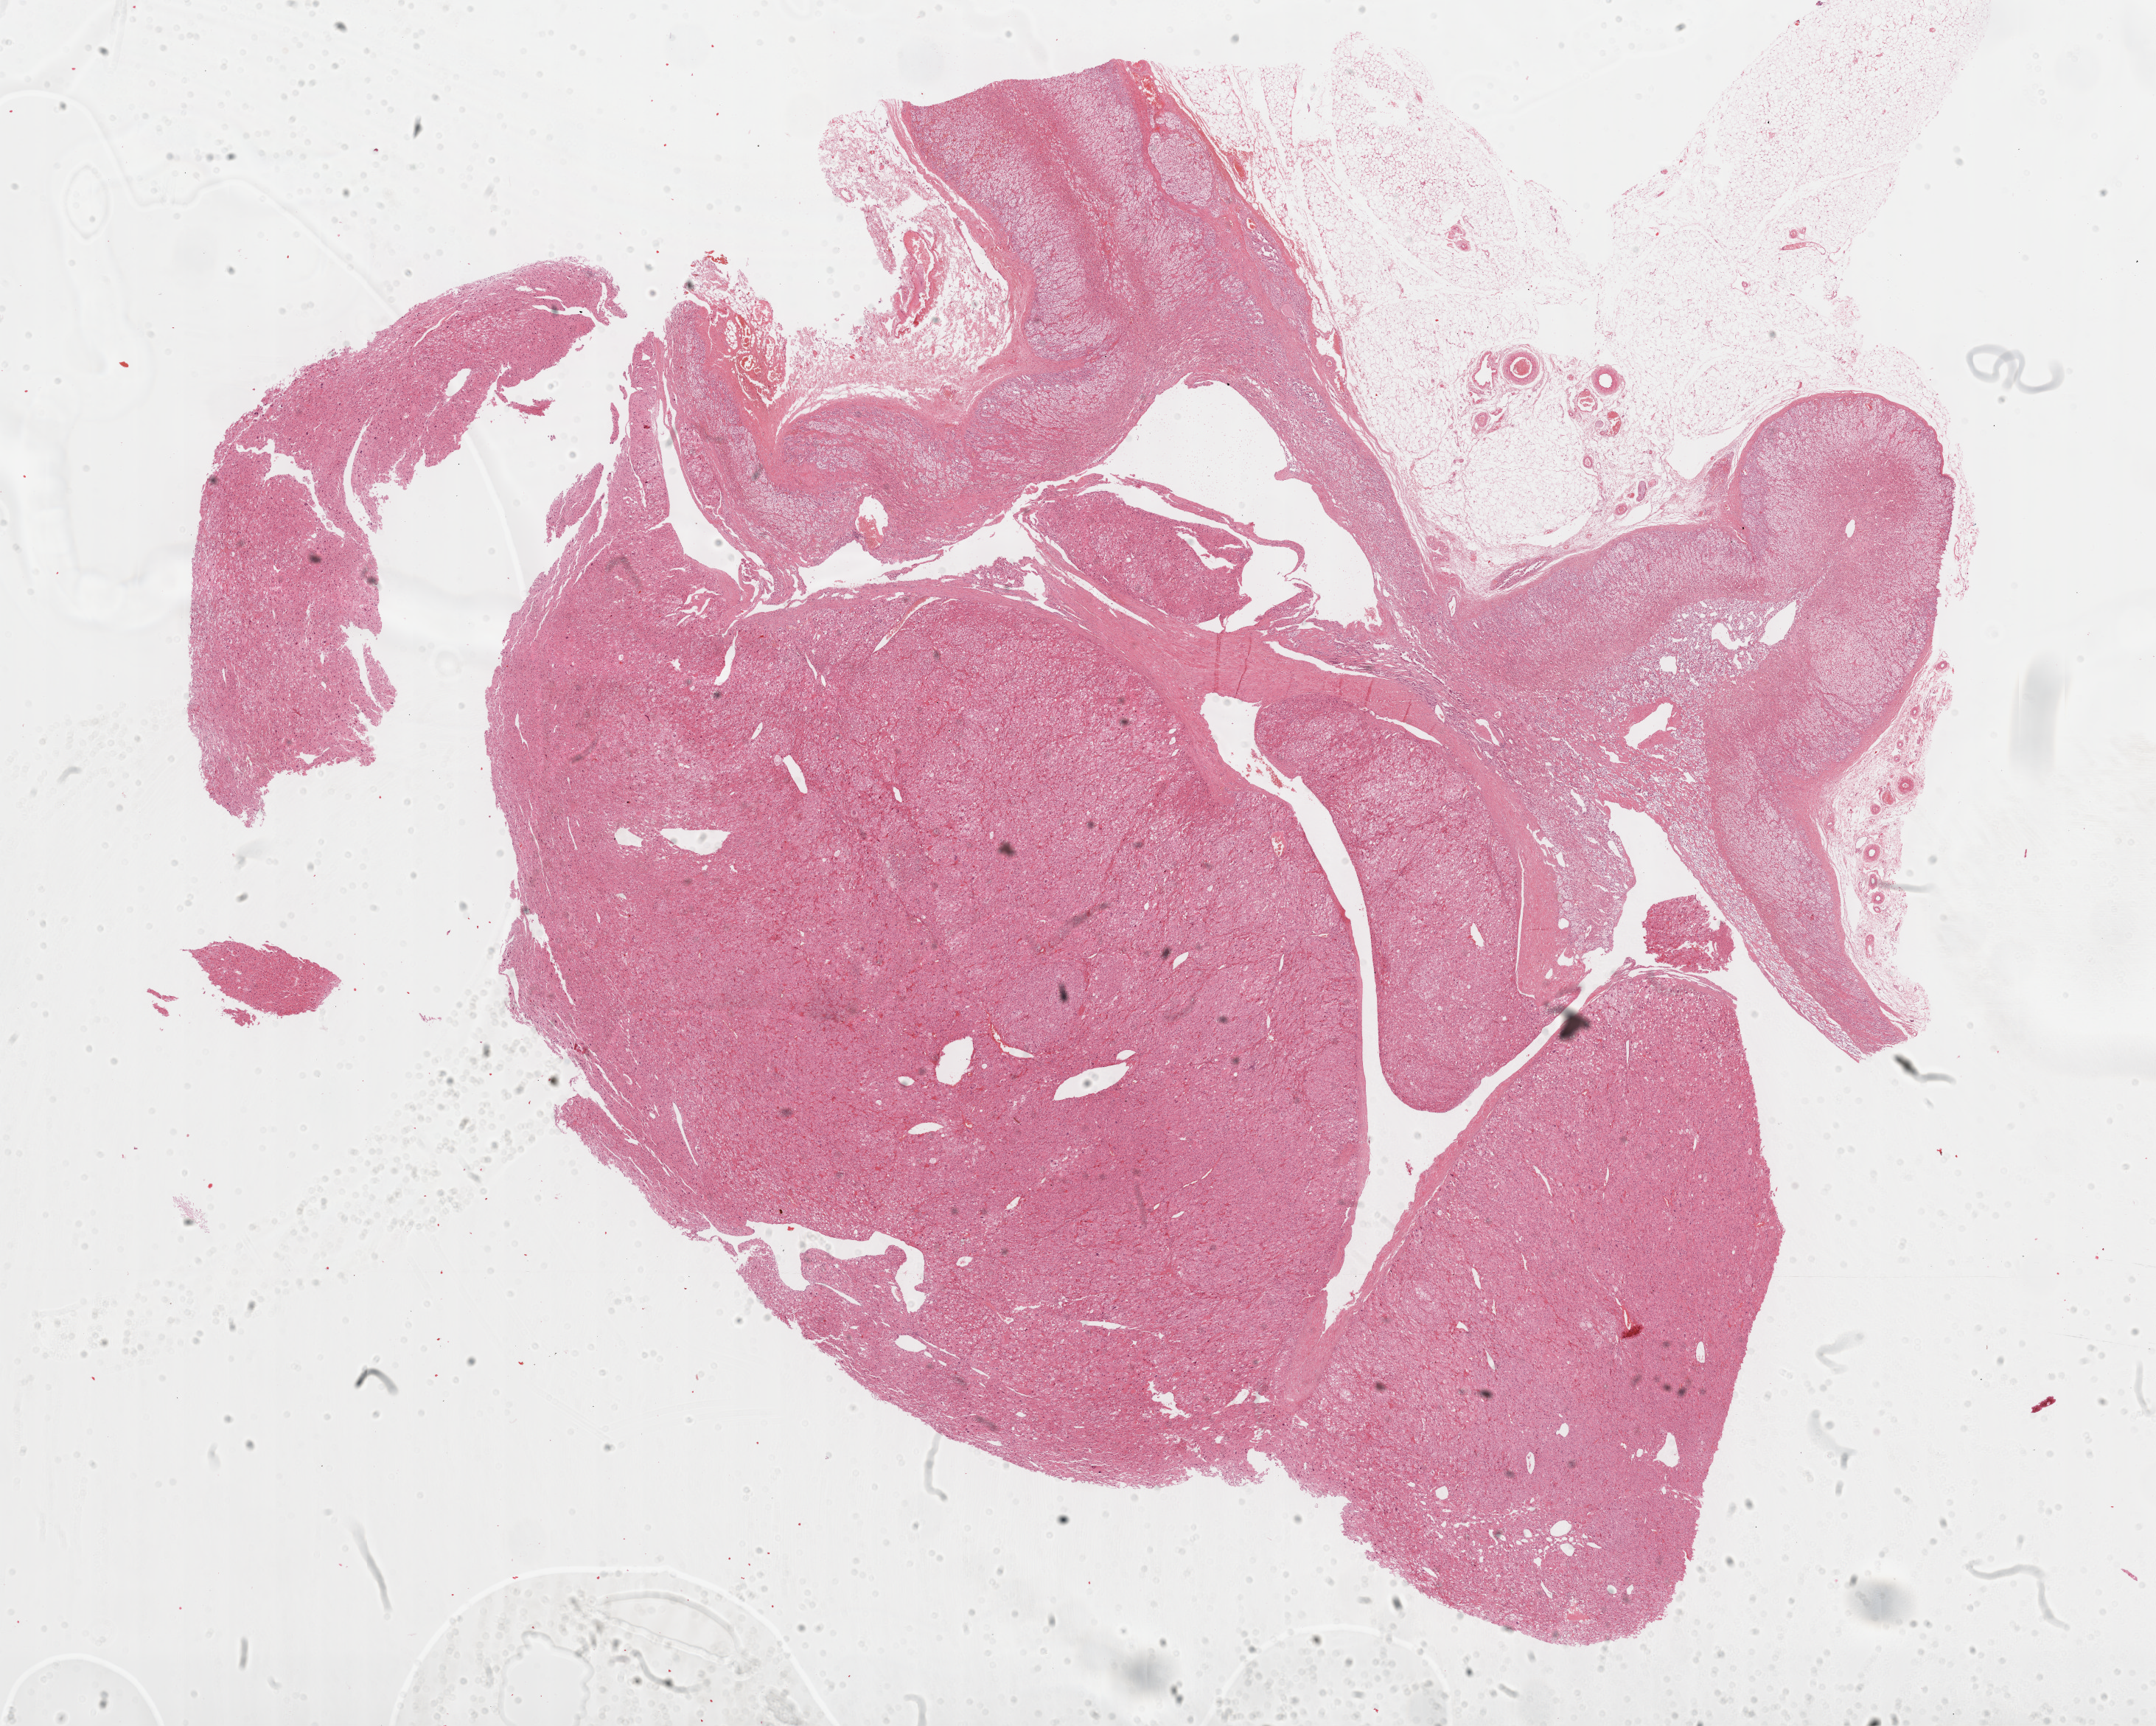
Whole-slide histology image, H&E, low-resolution overview of the scanned area, about 23.7 x 18.9 mm (acquisition: 40x scan); FFPE section; adrenal cortex, primary tumour sample. Female patient; age at initial diagnosis 36 years.
- diagnosis: Adrenal cortical carcinoma